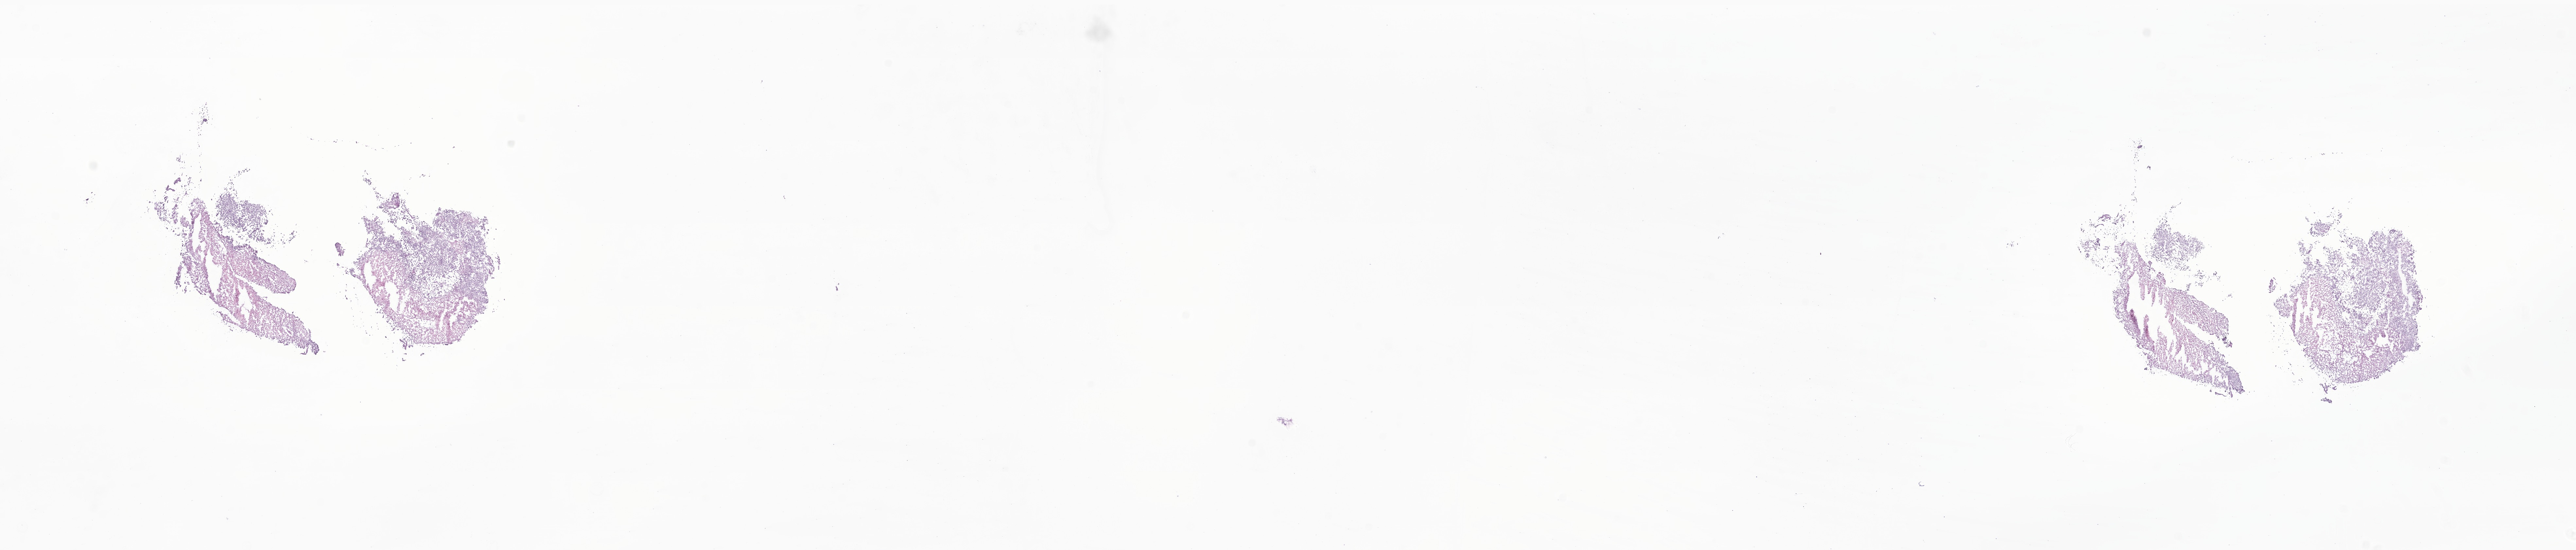
Digitized haematoxylin and eosin-stained section of tumor tissue from the cerebellum, shown as a low-resolution overview of the whole scanned area (about 33.2 x 7.1 mm), frozen section. Patient male; age 483 days (about 1.3 years).
Diagnosis (ICD-O-3 morphology term): Atypical teratoid/rhabdoid tumor.